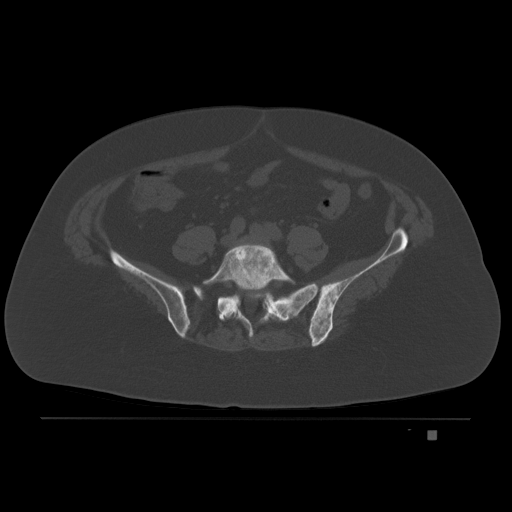
CT including the spine, one axial slice. Bone window (W 1800 / L 400 HU). 3 mm slice thickness. 512 × 512 image matrix, field of view 474 × 474 mm. Female patient, age 63 years. Case-level facts recorded for this patient, not image findings: primary cancer: breast.
Annotated regions visible in this slice (semi-automatically segmented with operator editing):
- L5 vertebra: bounding box (x1, y1, x2, y2) in pixels: (202, 243, 296, 320)